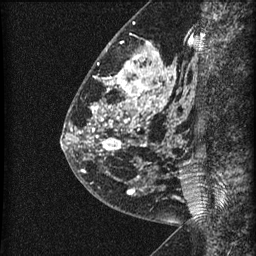
Breast MRI (dynamic contrast-enhanced), one sagittal slice; slice 22 of 60 in the series (ordered by position); dynamic contrast-enhanced series, image 2 of 3 at this slice position (ordered by acquisition); 1.5 T; TE 4.2 ms, TR 22.7 ms; 256 × 256 image matrix, field of view 180 × 180 mm. Female patient, age 48 years. From the clinical record (not read from this slice): setting: breast cancer imaged before/during neoadjuvant chemotherapy; receptor status: triple-negative.
Outlined on this slice (semi-automatic segmentation, software-assisted and operator-edited):
- analysis volume of interest (the breast-tissue region the enhancement analysis was run in; not a lesion): bounding box [x1, y1, x2, y2] px = [81, 23, 186, 202]
- tumour enhancement mask (voxels above the 90 % enhancement threshold inside the analysis volume of interest): [83, 50, 173, 180]